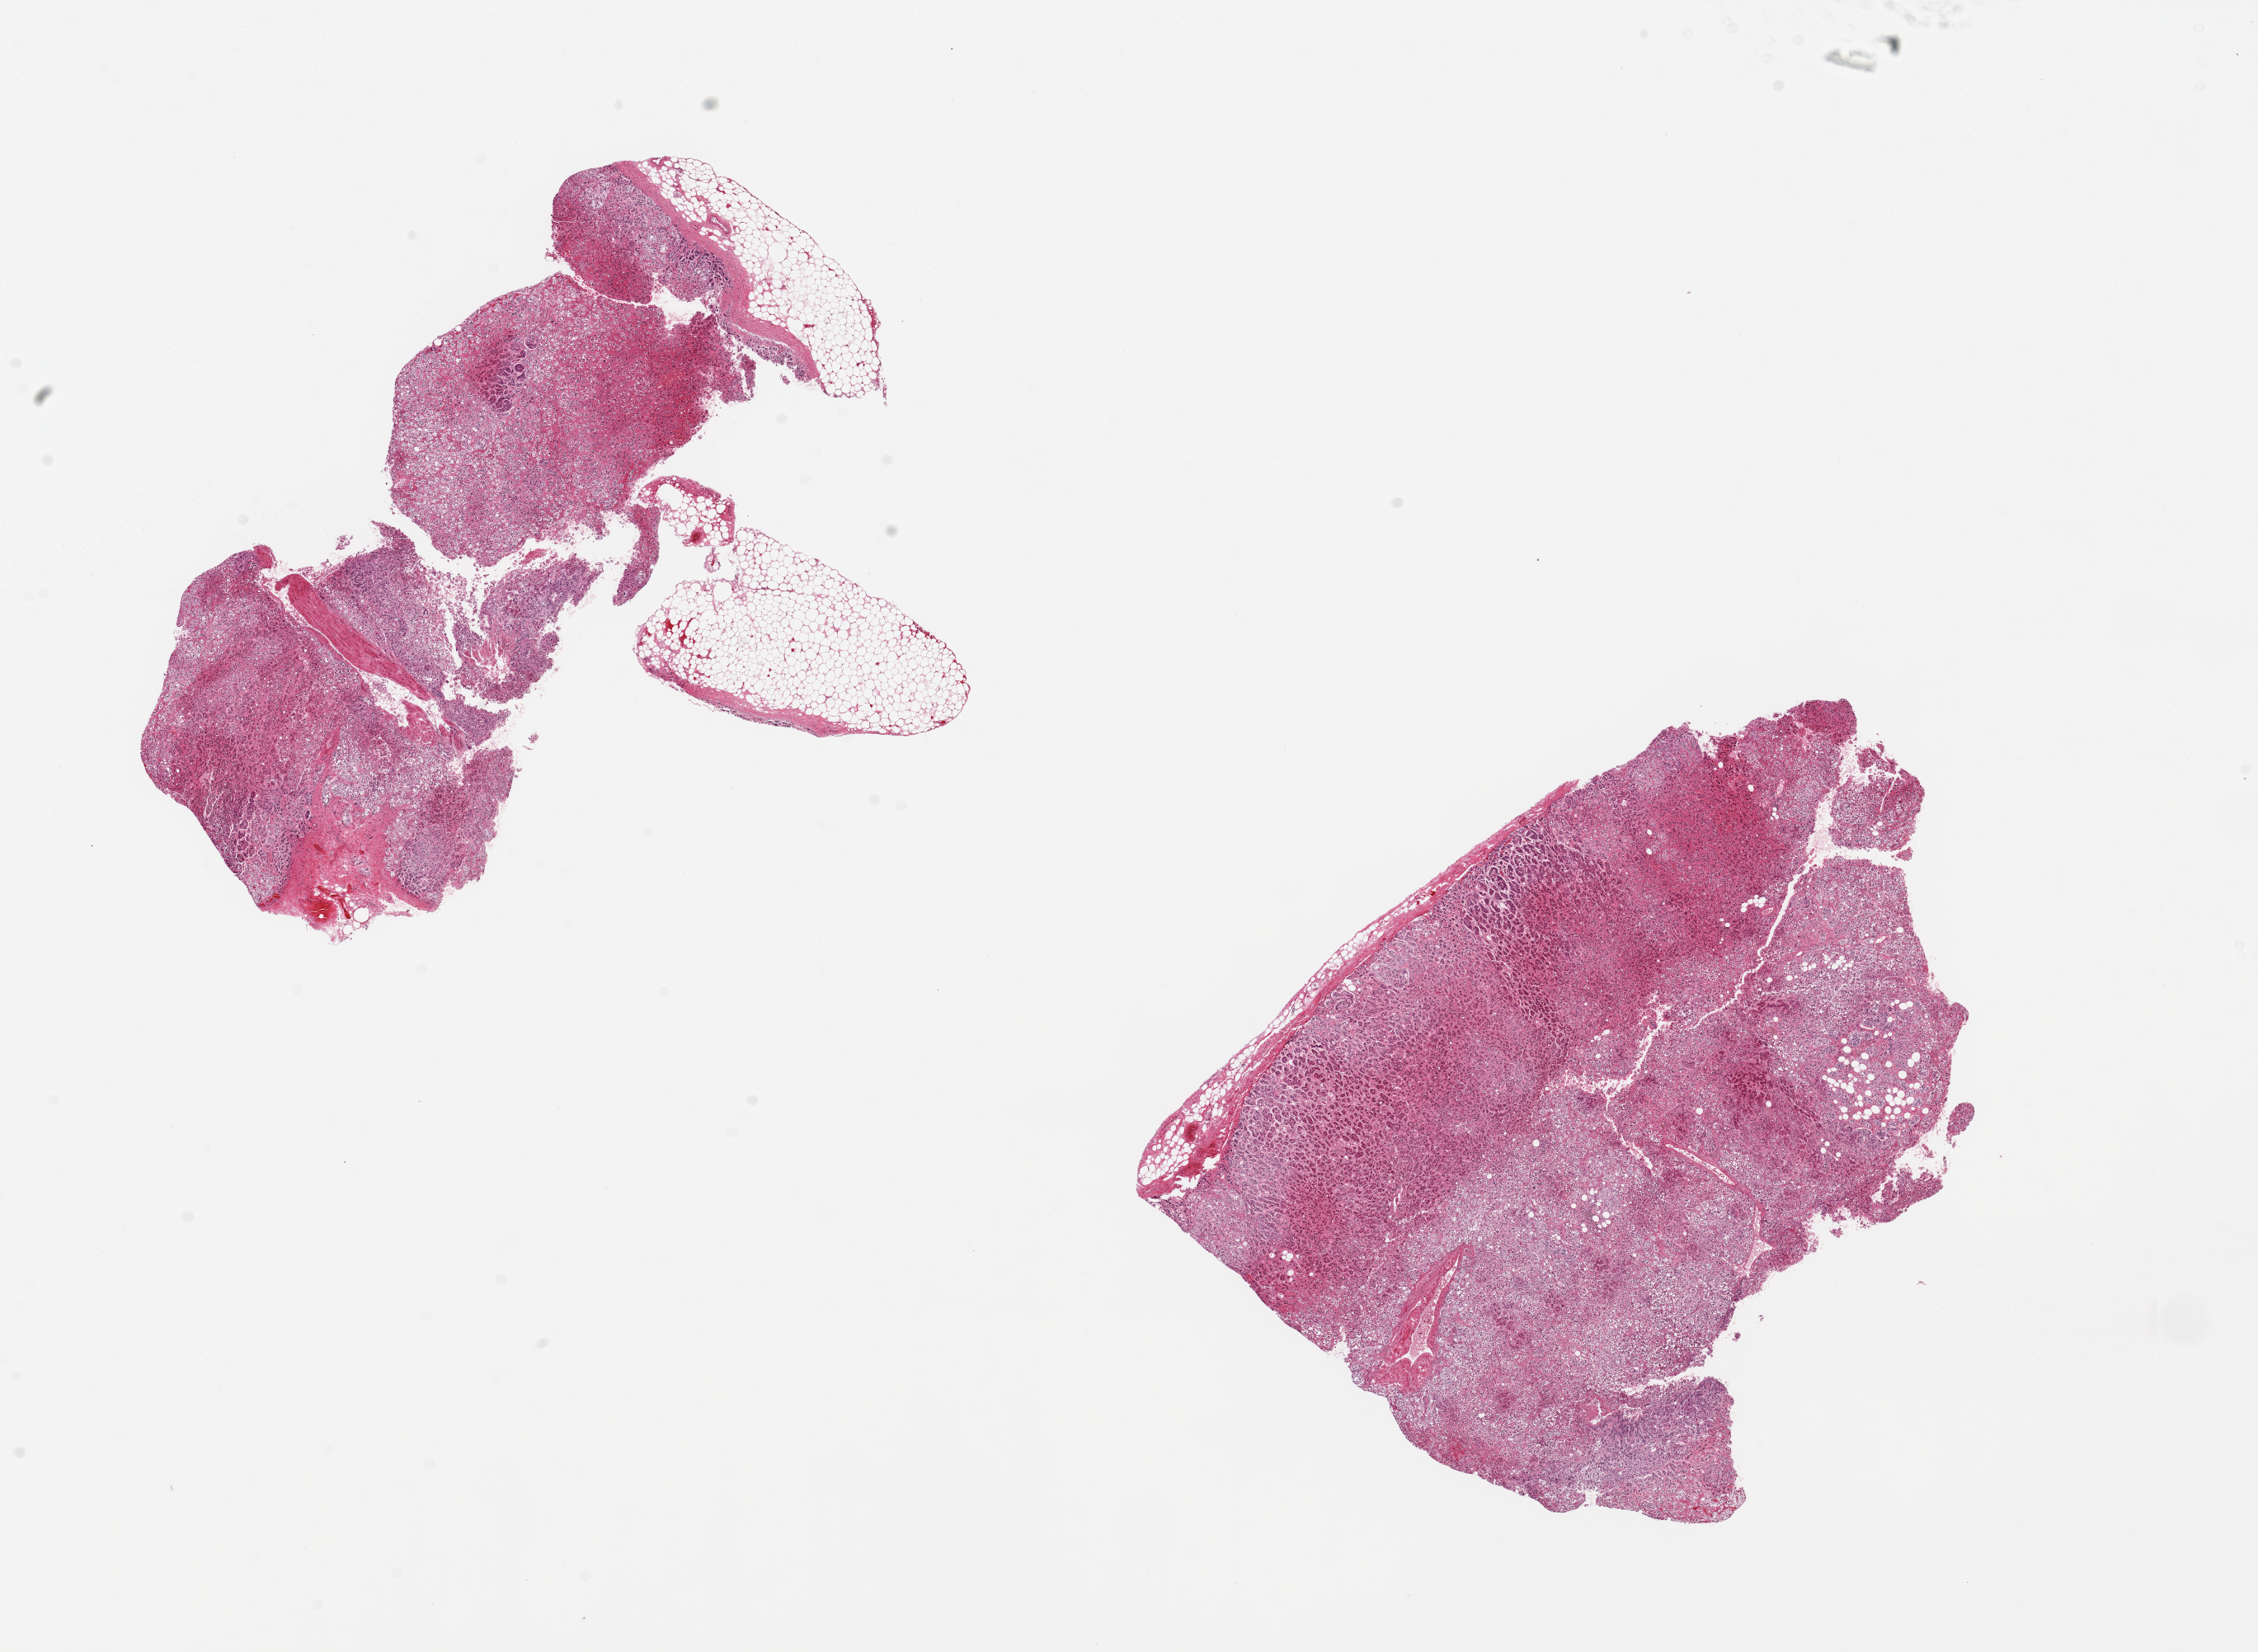
Digitized hematoxylin and eosin (H&E)-stained section, low-resolution overview of the scanned area, about 21.7 x 15.8 mm (from a 20x scan); PAXgene-fixed paraffin-embedded (PFPE) section; sampled site (target tissue): adrenal gland; donor tissue sample.
Pathologist's review note for this sample: 2 pieces. 8x6 & 8x7mm; smaller piece has 2.5x 1.5 mm and 3 x0.8 mm external adipose.